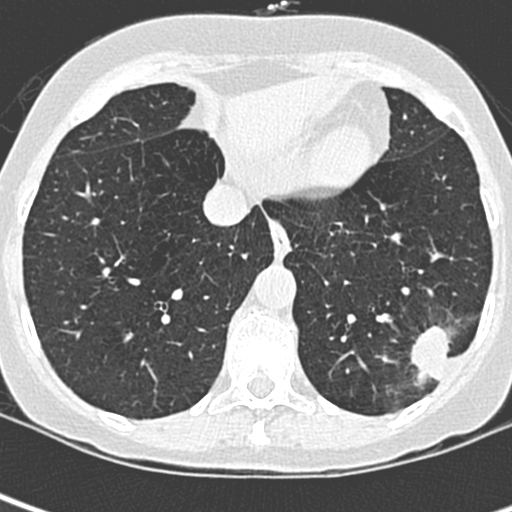
Low-dose screening chest CT, one axial slice; slice 83 of 252 in the series (ordered by position); 120 kVp; lung window (W 1500 / L -600 HU); 1.3 mm slice thickness; 512 × 512 image matrix.
Outlined on this slice (outlined manually by an expert reader):
- lesion 1 (tumor, lower lobe of left lung): bounding box [x1, y1, x2, y2] px = [411, 325, 459, 389]